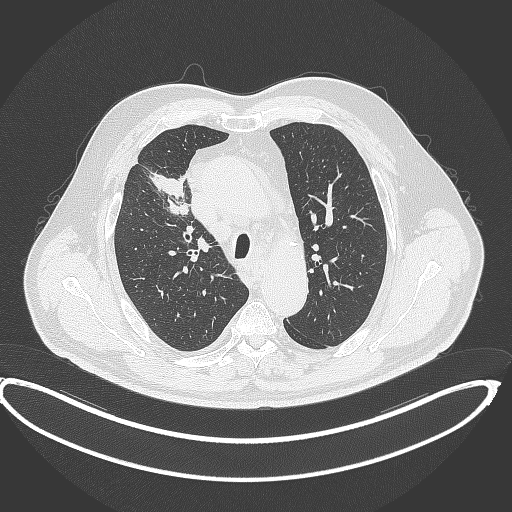
Chest CT, one axial slice; slice 293 of 390 in the series (ordered by position); 120 kVp; lung window (W 1500 / L -600 HU); 512 × 512 image matrix. Male patient, age 62 years. From the clinical record (not read from this slice): clinical TNM (as recorded): T1c N3 M1c.
Structures marked on this image (bounding box drawn by a radiologist):
- lung tumour (recorded histology: adenocarcinoma): bounding box (x1, y1, x2, y2) in pixels: (146, 170, 191, 215)